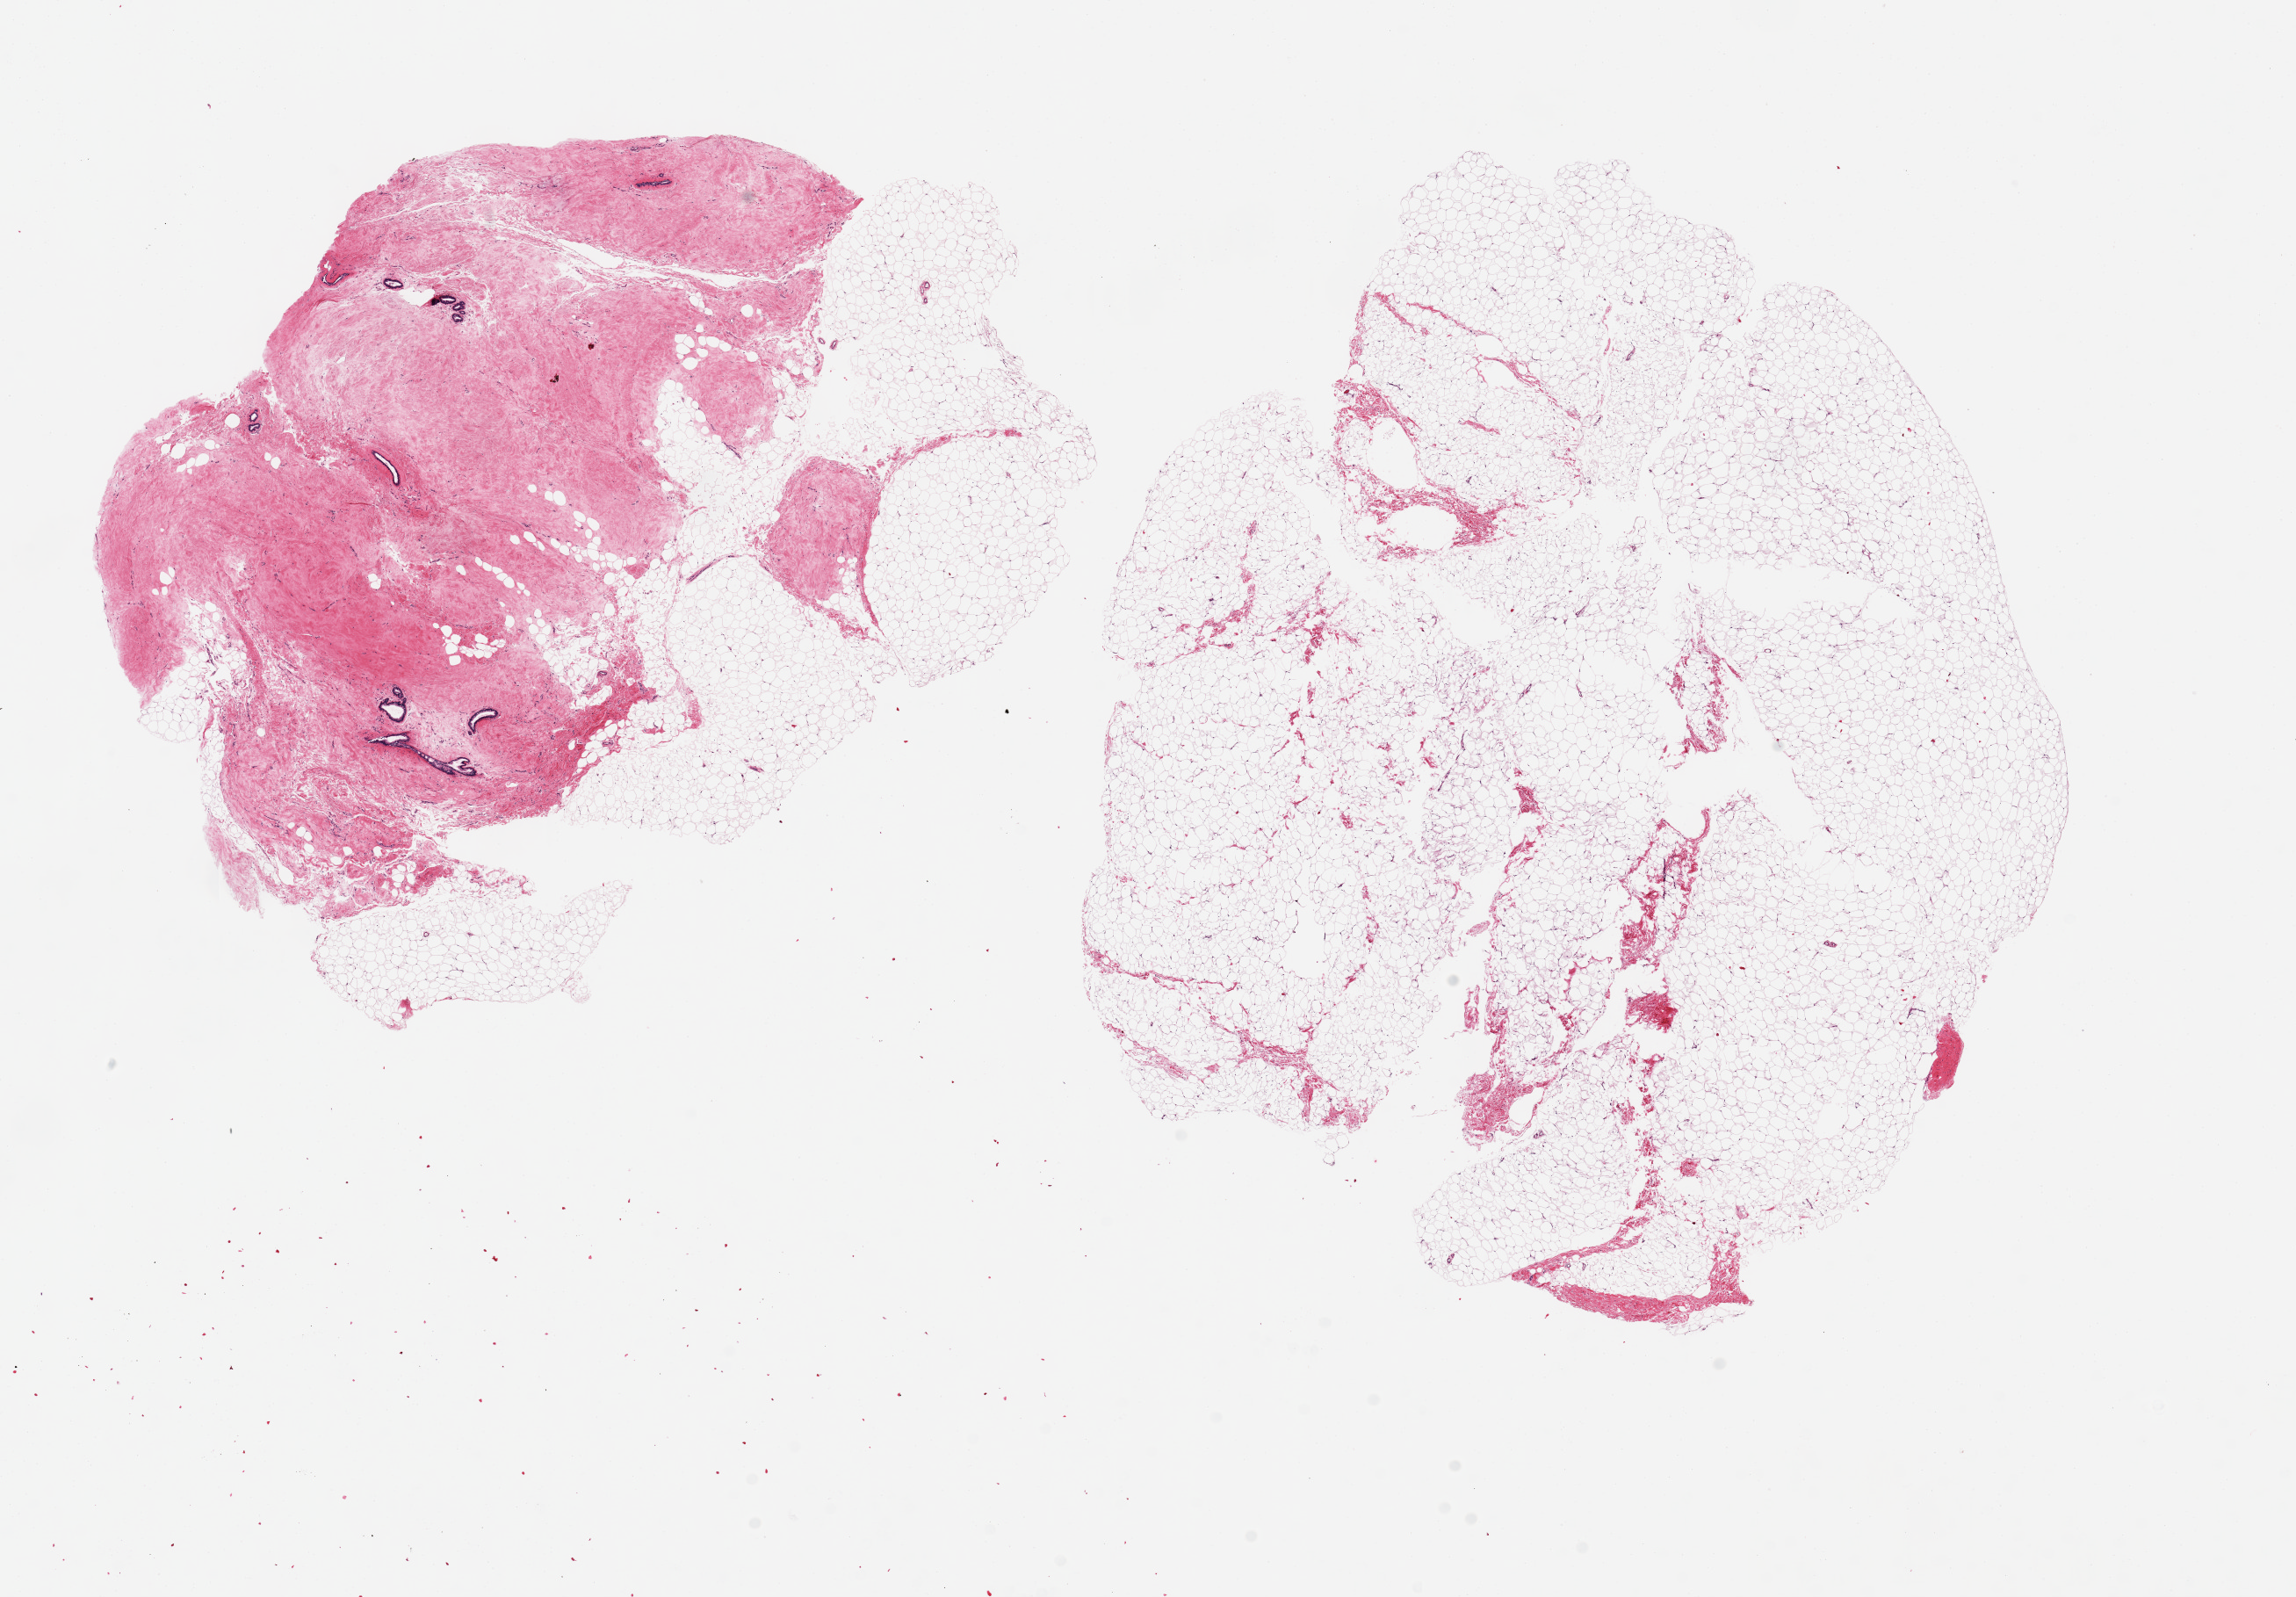
Hematoxylin and eosin (H&E) whole-slide image, low-resolution overview of the scanned area, about 20.7 x 14.4 mm, PAXgene-fixed paraffin-embedded (PFPE) section, sampled site (target tissue): breast, donor tissue sample. Male donor.
Pathologist's review note for this sample: 2 pieces, 9x7 & 11x9mm; 1 piece is fibroadipose with mammary ducts, mild gynecomastia; other piece is all adipose.